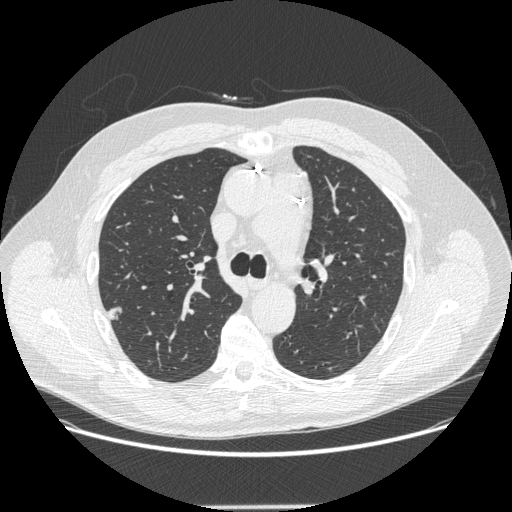
Chest CT (low-dose screening protocol), one axial image. Third annual screen. Lung window (W 1500 / L -600 HU). 1.25 mm slice thickness. Standard (soft-tissue) reconstruction kernel (STANDARD). Slice 77 of 265 in the series. 512 × 512 image matrix. Male participant, aged 62 years at enrolment.
- Expert-annotated lung lesion, bounding box [x1, y1, x2, y2] px = [94, 298, 133, 335].
- The exam's reader record, not a measurement of the box and not confirmed to be the same lesion: non-calcified nodule or mass ≥4 mm, right upper lobe, 12 × 11 mm, smooth margins, soft tissue attenuation, pre-existing on the prior screen: yes; interval growth: yes.
- Official screen result: positive, other.